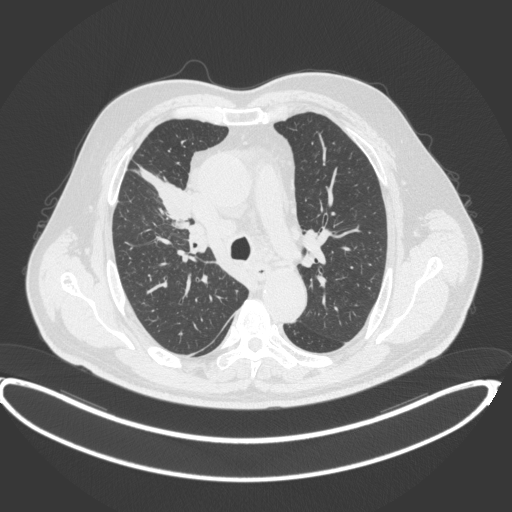
Chest CT, one axial slice; position 278 of 395 along the scan axis; 120 kVp; lung window (W 1500 / L -600 HU); 1 mm slice thickness; 512 × 512 image matrix, field of view 448 × 448 mm. Patient: male, 62 years. Case-level facts recorded for this patient, not image findings: clinical TNM (as recorded): T1c N3 M1c.
Structures marked on this image (rectangle marked by the reading radiologist):
- lung tumour (recorded histology: adenocarcinoma): bounding box (x1, y1, x2, y2) in pixels: (133, 164, 192, 223)